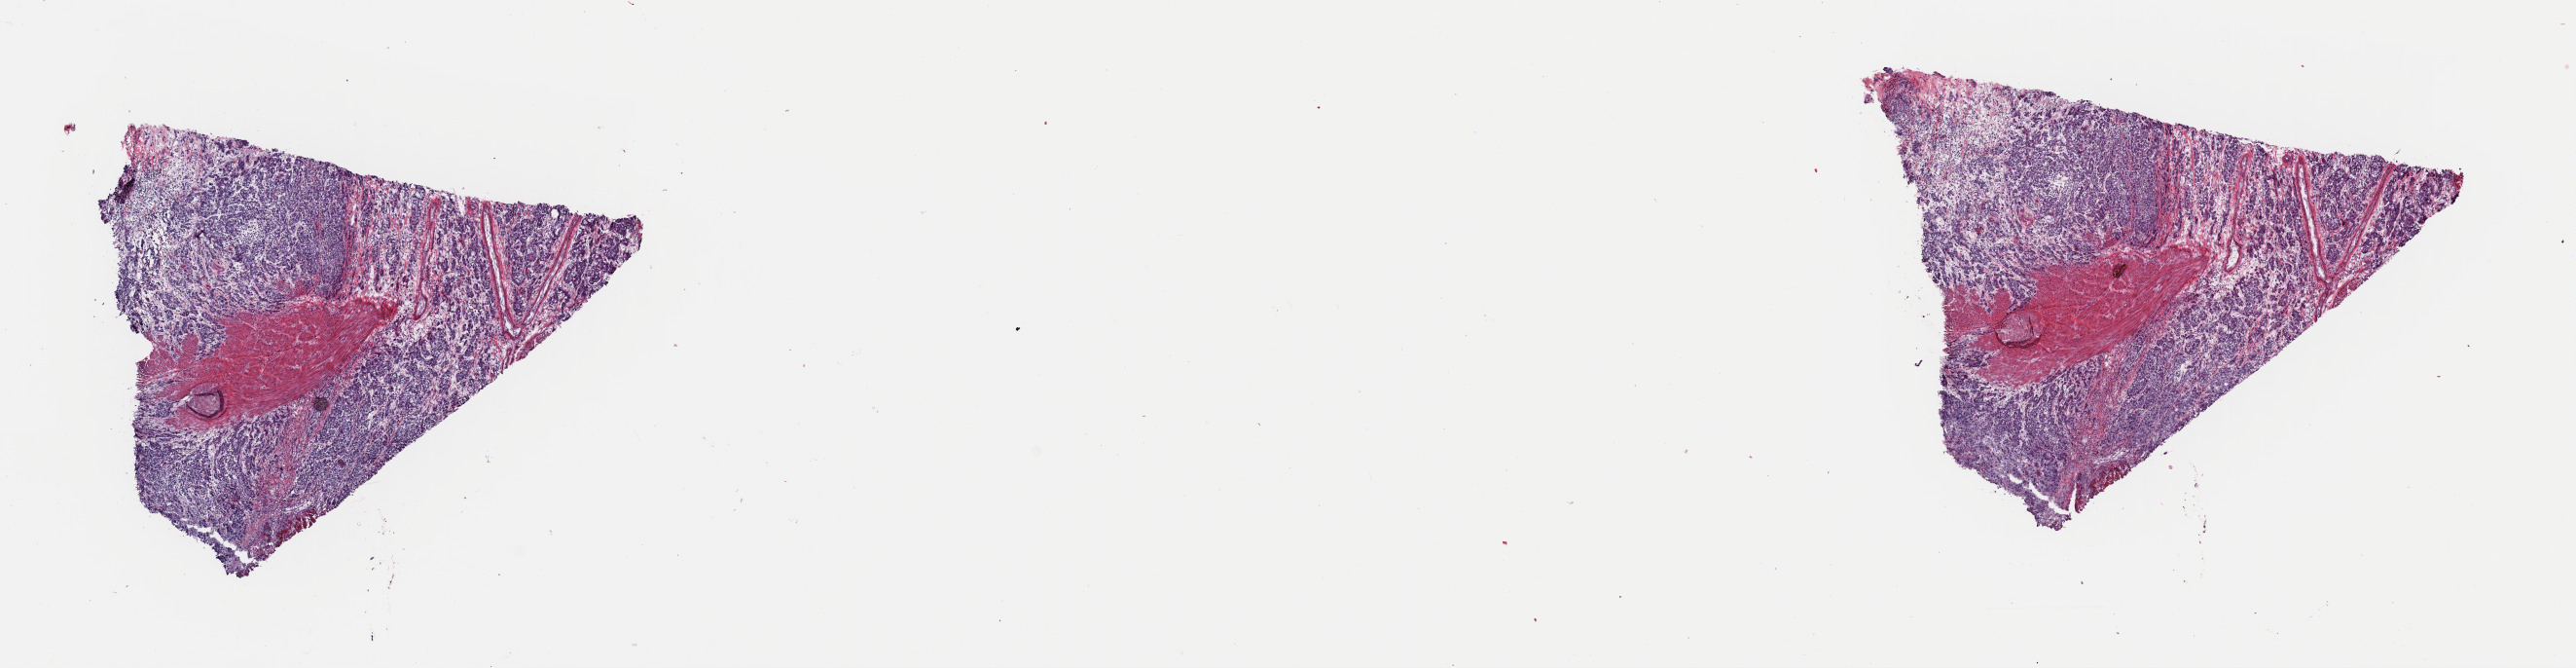
H&E whole-slide image — a low-resolution overview of the entire scanned area, about 20.9 x 5.4 mm (slide scanned at 40x). Frozen section from the top of the tissue portion. Bladder, primary tumour sample. Male, age 76 years at initial diagnosis. Slide review estimates, as recorded: tumour cells 70%, tumour nuclei 70%.
Pathologic diagnosis: Transitional cell carcinoma.